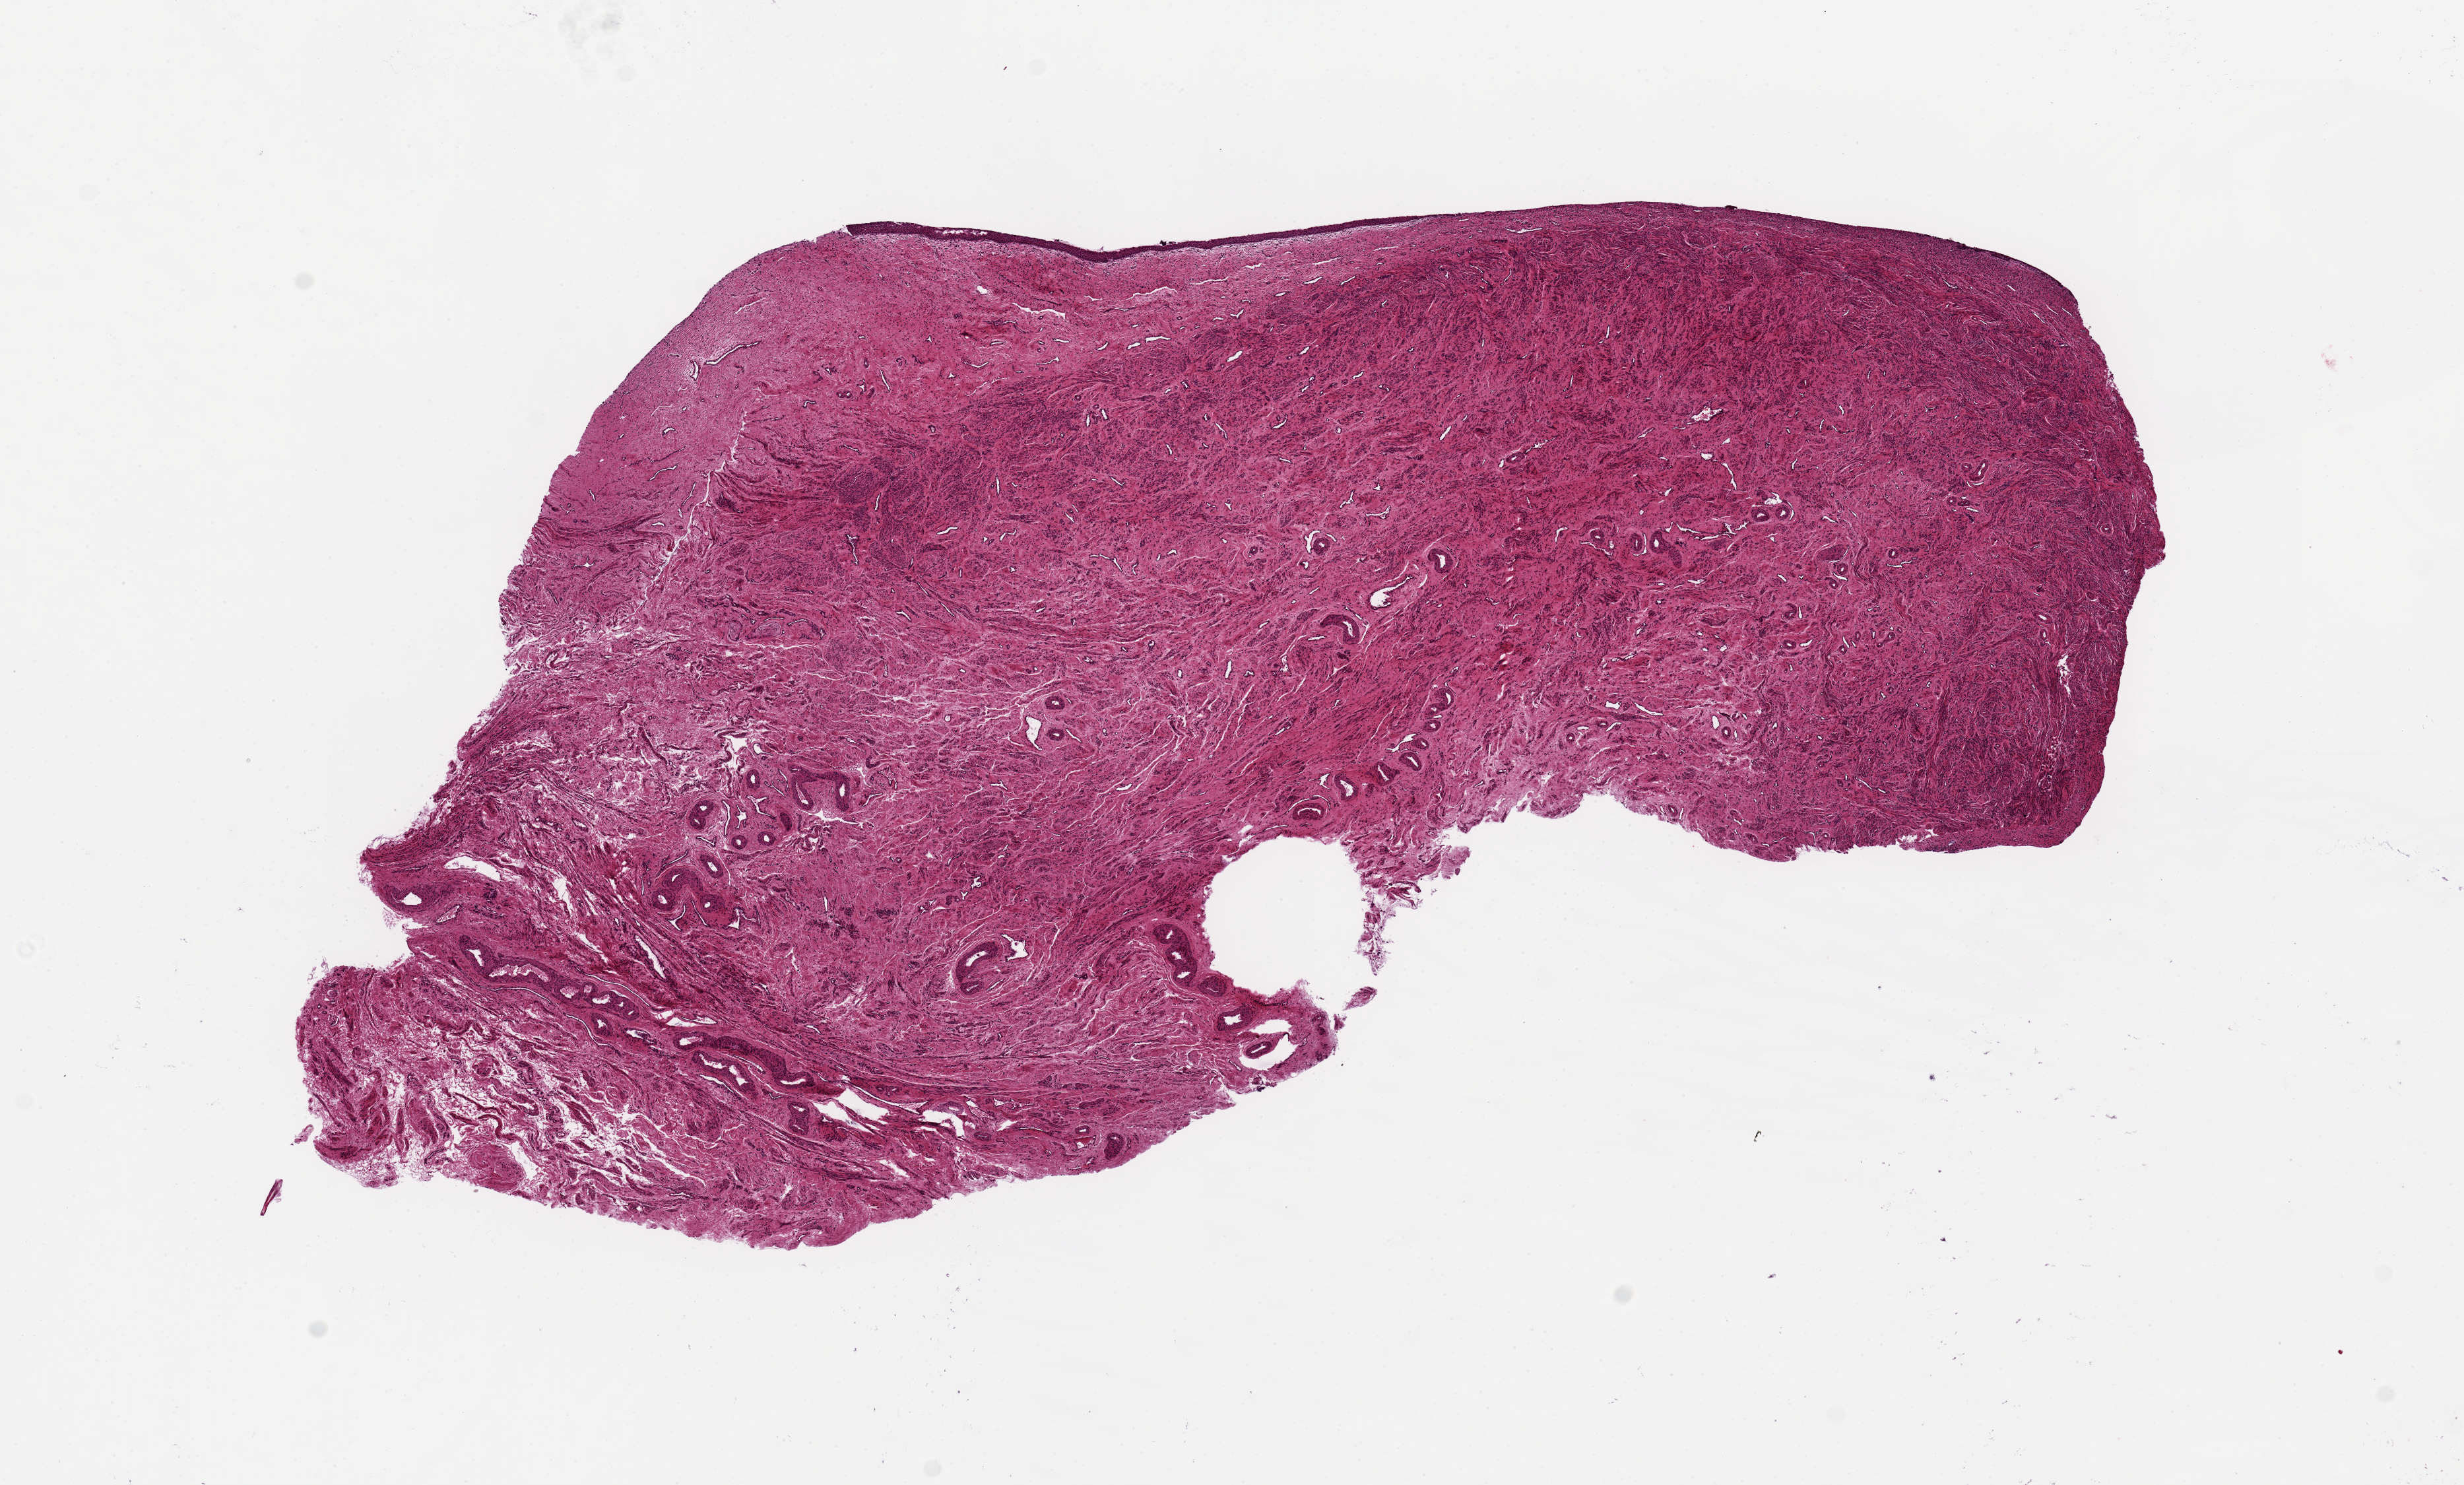
Whole-slide image, H&E stain, low-resolution overview of the scanned area, about 14.8 x 8.9 mm (from a 20x scan). PAXgene-fixed paraffin-embedded (PFPE) section. Sampled site (target tissue): exocervix. Donor tissue sample. Donor: female.
Reviewer comment on this tissue sample: ~10x3.5mm. No endocervical glands. 55m thick edge of sqaumous mucosa on one edge, ~1.5% of thickness1.3.